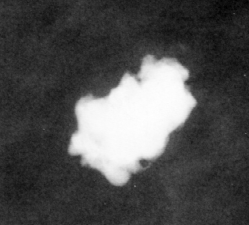
Crop from a digitized film mammogram around one marked abnormality; right breast; MLO view; BI-RADS breast density category 4 (scale 1–4).
Calcifications, morphology coarse; BI-RADS assessment category 2; benign; no additional work-up was recommended (benign without callback).